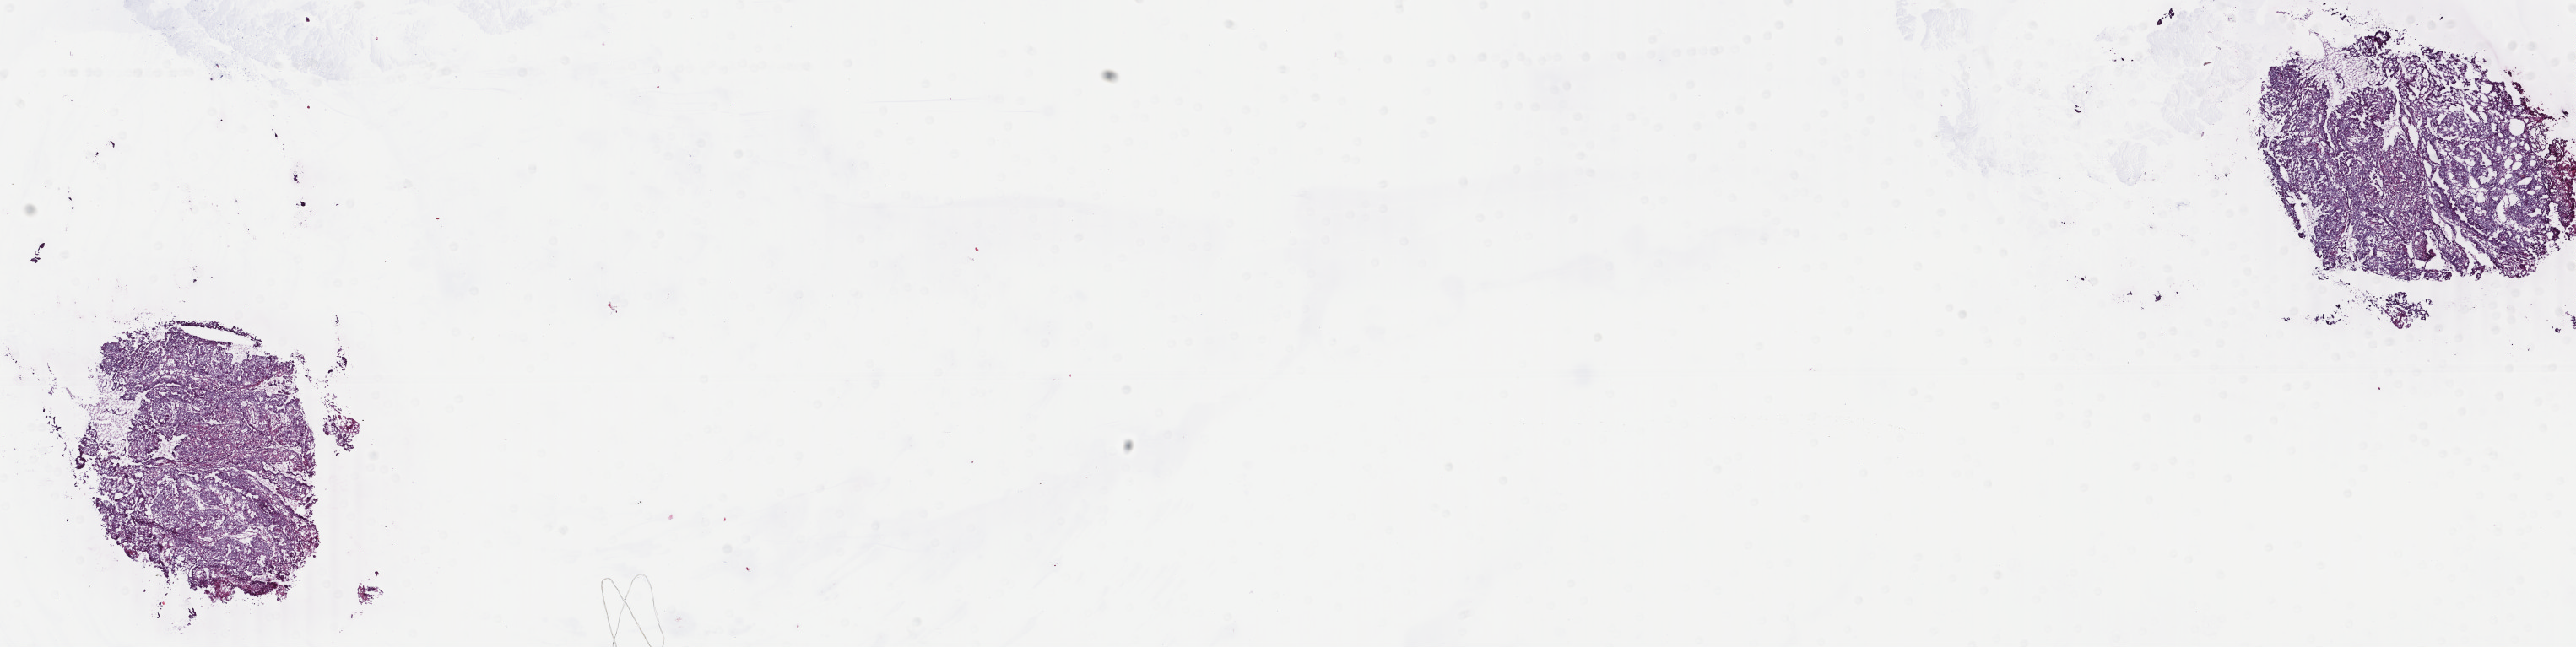
Hematoxylin and eosin (H&E) stained whole-slide image — a low-resolution overview of the entire scanned area, about 24.3 x 6.1 mm (acquisition: 40x scan); frozen section from the top of the tissue portion; sample: primary tumour, rectum. Male patient; age at initial diagnosis 35 years. Slide review estimates, as recorded: tumour cells 80%, tumour nuclei 80%, normal cells 0%, stromal cells 18%, necrosis 2%. Infiltration values recorded for this section: lymphocyte infiltration 4%, monocyte infiltration 4%, neutrophil infiltration 1%.
* lymph nodes positive (case pathology): 0 of 34 examined
* diagnosis: Adenocarcinoma, NOS
* AJCC pathologic stage: I